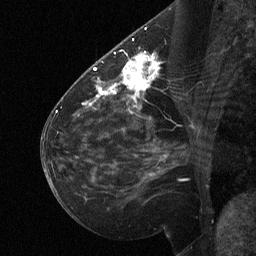
Breast MRI (dynamic contrast-enhanced), one sagittal slice; position 31 of 64 along the scan axis; dynamic contrast-enhanced study with each time point stored as its own series, time point 2 of 3 at this slice position (early post-contrast, ordered by acquisition time); 1.5 T; TE 4.8 ms, TR 27 ms; 2 mm slice thickness; 256 × 256 image matrix, field of view 200 × 200 mm. Female patient, age 51 years. Case-level facts recorded for this patient, not image findings: setting: breast cancer imaged before/during neoadjuvant chemotherapy; receptor status: HR-positive, HER2-negative.
Annotated regions visible in this slice (semi-automatically segmented with operator editing):
- analysis volume of interest (the breast-tissue region the enhancement analysis was run in; not a lesion): box from (x=112, y=46) to (x=169, y=106) px
- tumour enhancement mask (voxels above the 90 % enhancement threshold inside the analysis volume of interest): (x=112, y=53)–(x=158, y=100)